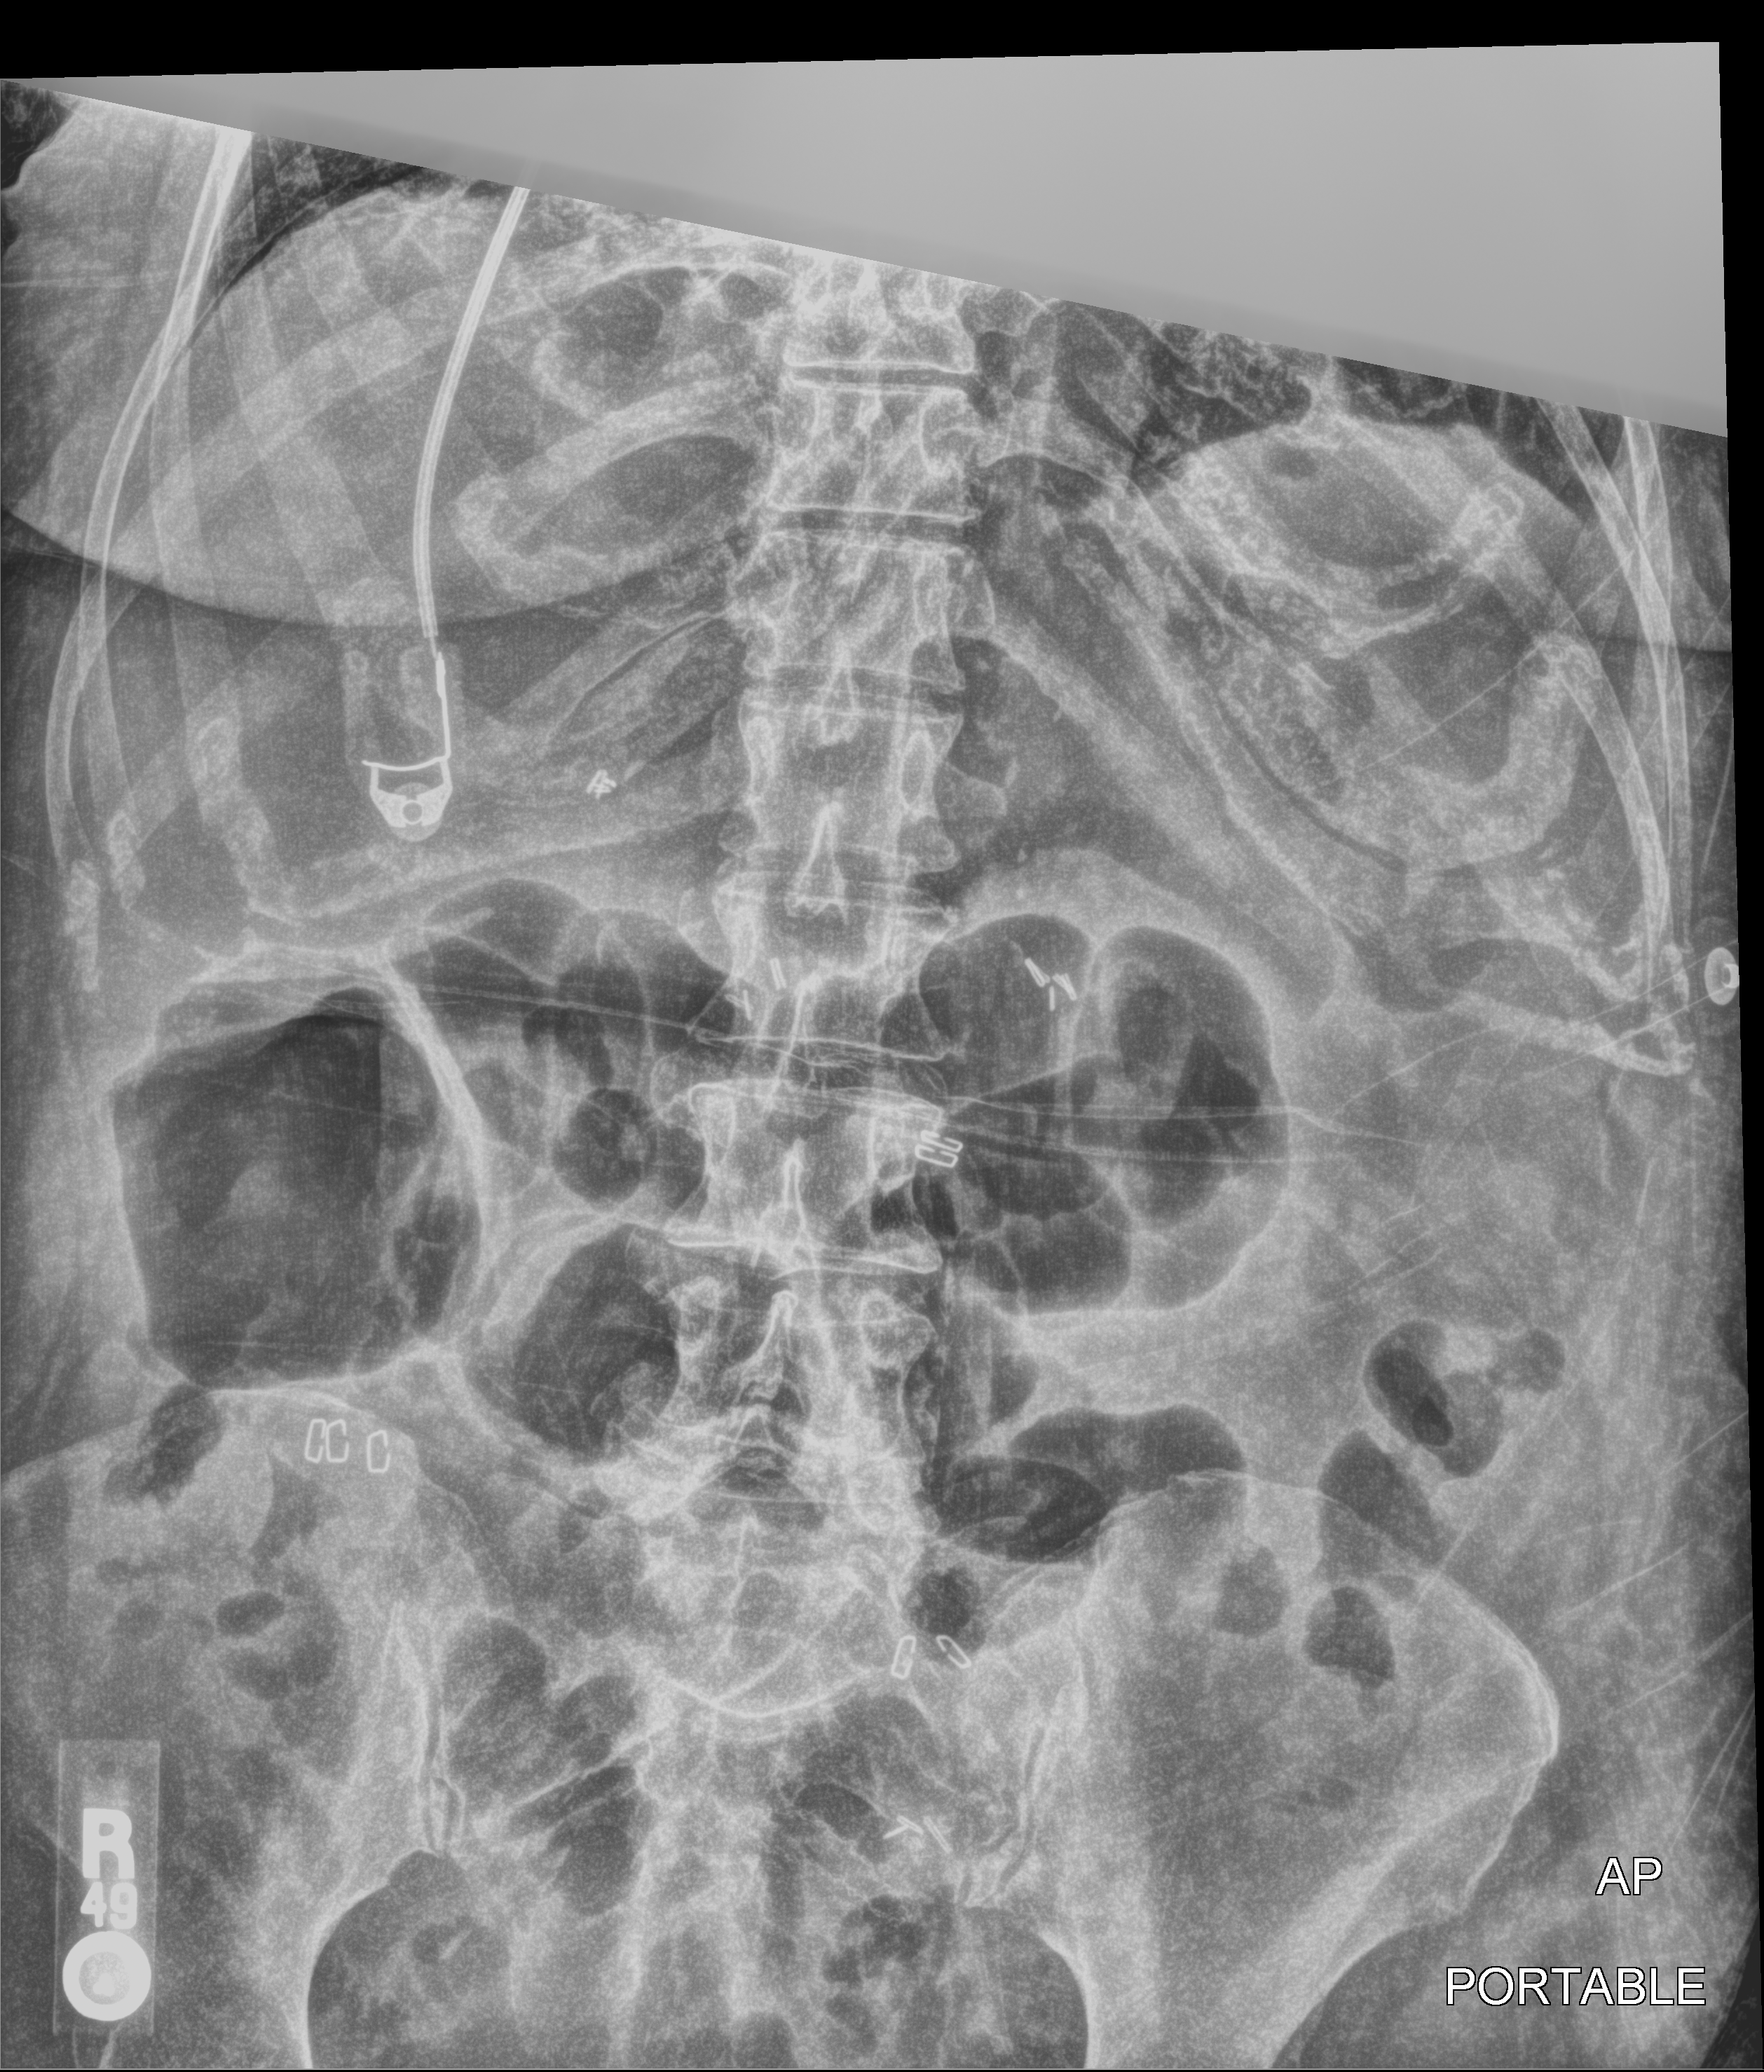
Abdomen X-ray (portable); anteroposterior (AP) projection. Female patient hospitalised with COVID-19, age 18–59 years.
Admission-level facts for this patient (not findings on this image; timing relative to this image not recorded):
- mechanically ventilated during this hospital stay: no
- admitted to intensive care during this hospital stay: no